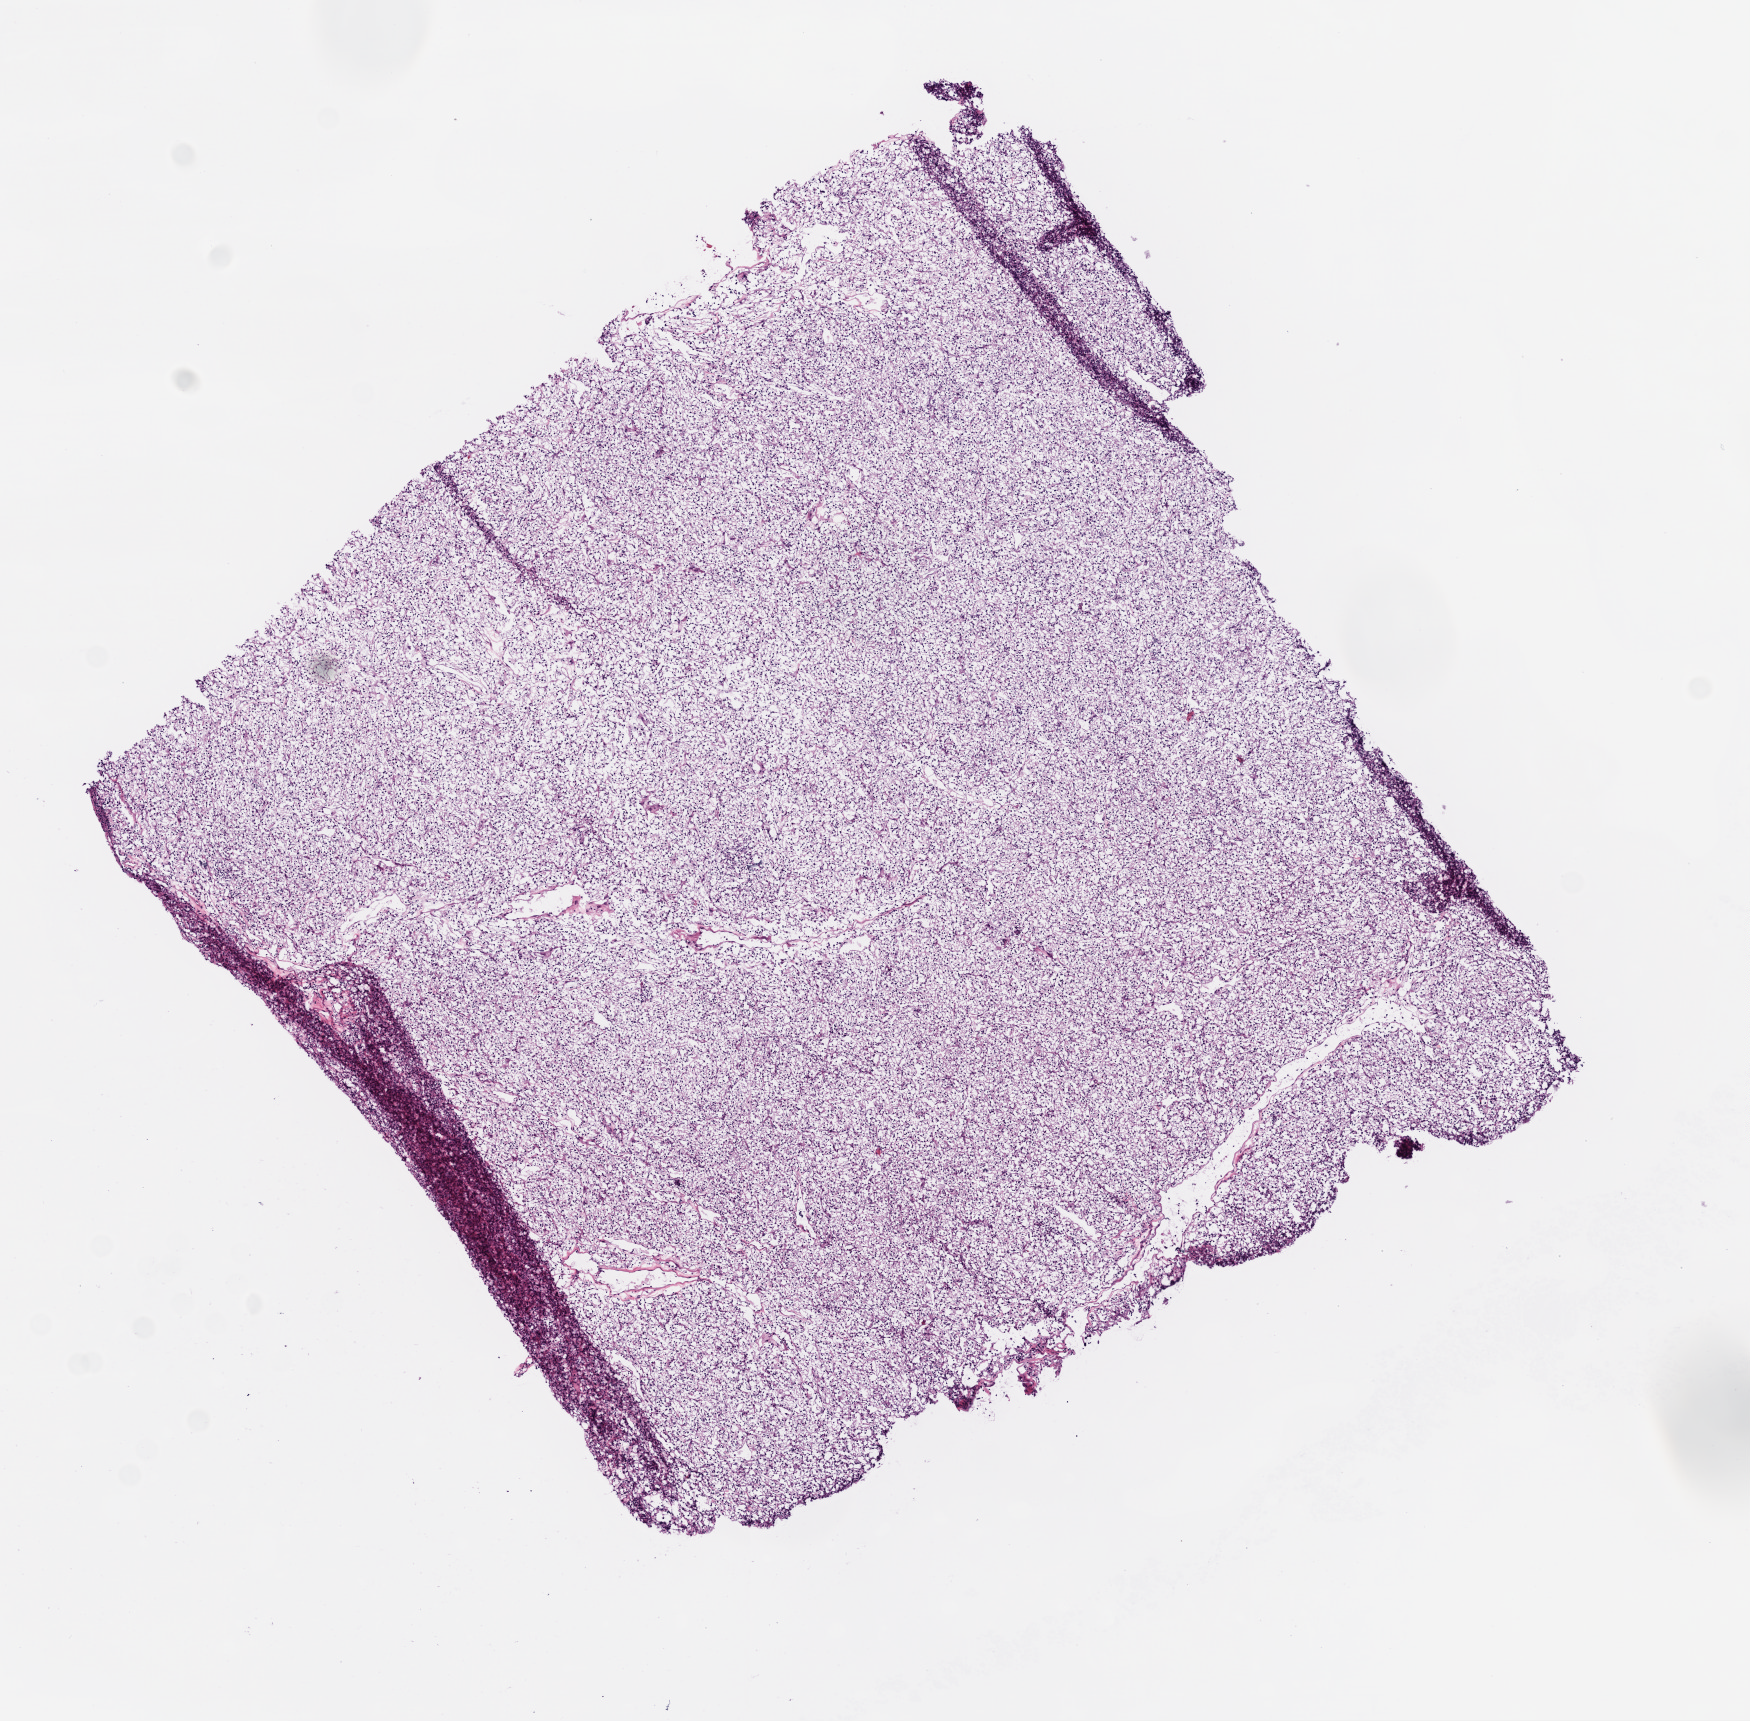
Digitized Hematoxylin and eosin (H&E) stained tissue section (whole slide), a low-resolution overview of the entire scanned area, about 7.0 x 6.9 mm (from a 20x scan), frozen section, sample: primary tumour, kidney. Male, age 79 years at initial diagnosis. Histologic grade: G3 (poorly differentiated). Pathologist review of this section (percent, as recorded): tumour cells 95%, tumour nuclei 80%, normal cells 0%, stromal cells 5%, necrosis 0%. Infiltration values recorded for this section: lymphocyte infiltration 15%, monocyte infiltration 0%, neutrophil infiltration 0%.
- pathologic diagnosis: Clear cell adenocarcinoma, NOS
- TNM: T2 N0 M0
- AJCC pathologic stage: II